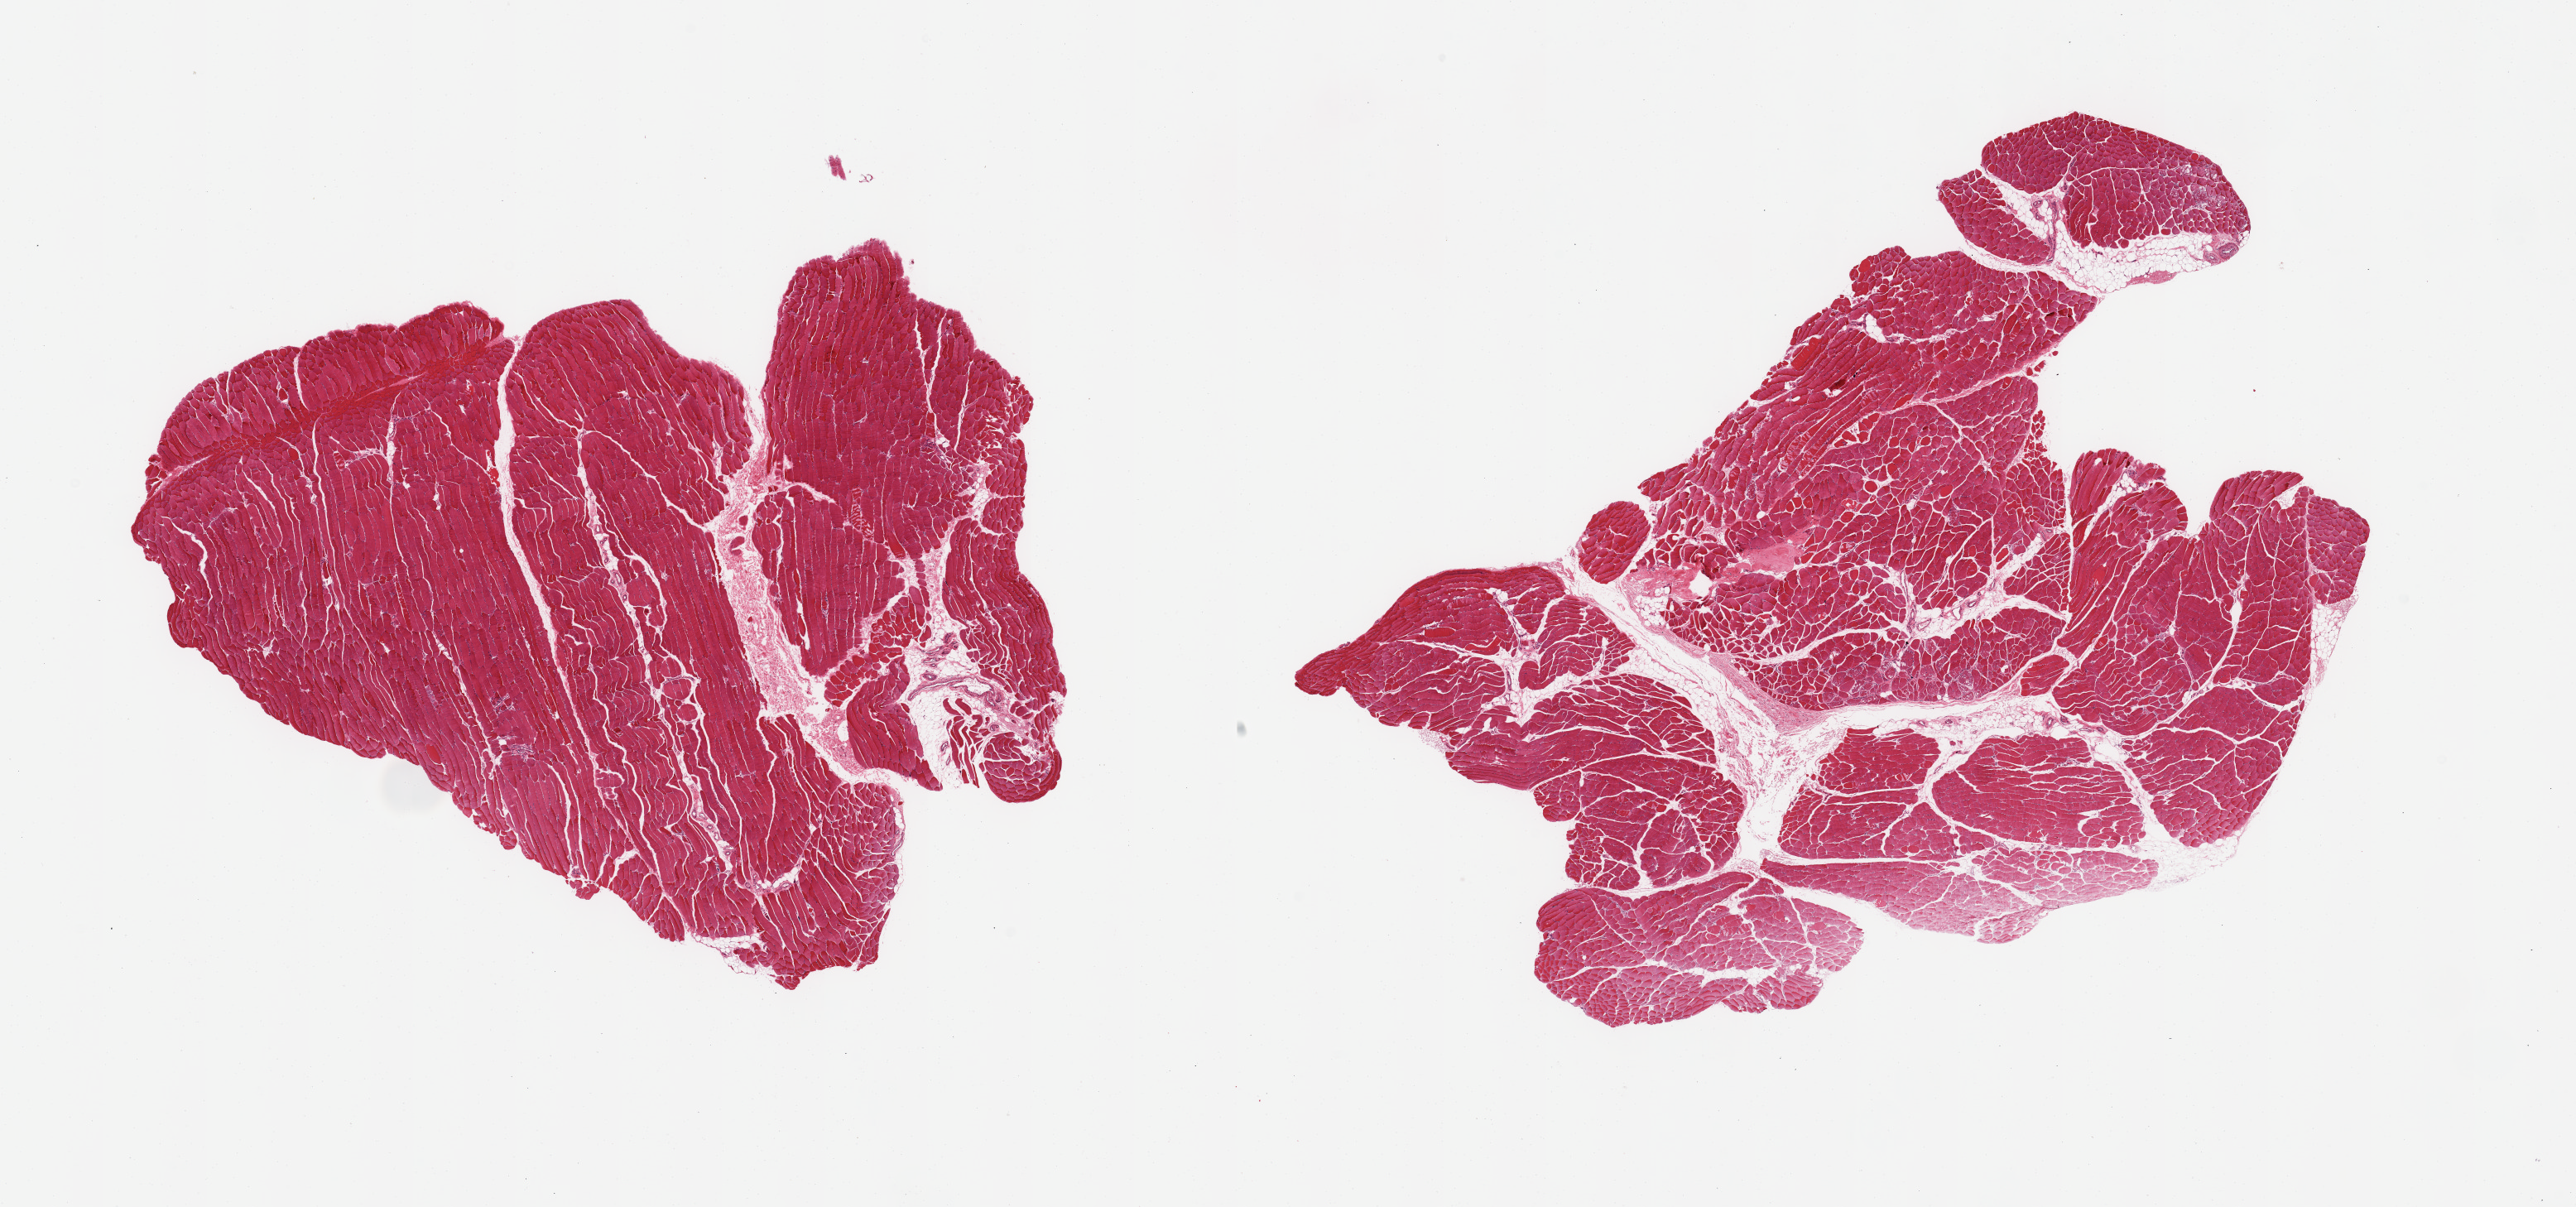
Whole-slide image, haematoxylin and eosin stain, a low-resolution overview of the entire scanned area, about 24.6 x 11.5 mm. PAXgene-fixed paraffin-embedded (PFPE) section. Sampled site (target tissue): skeletal muscle. Tissue donor sample. Female donor.
Pathologist's review note for this sample: 2 pieces; mild to moderate autolysis.